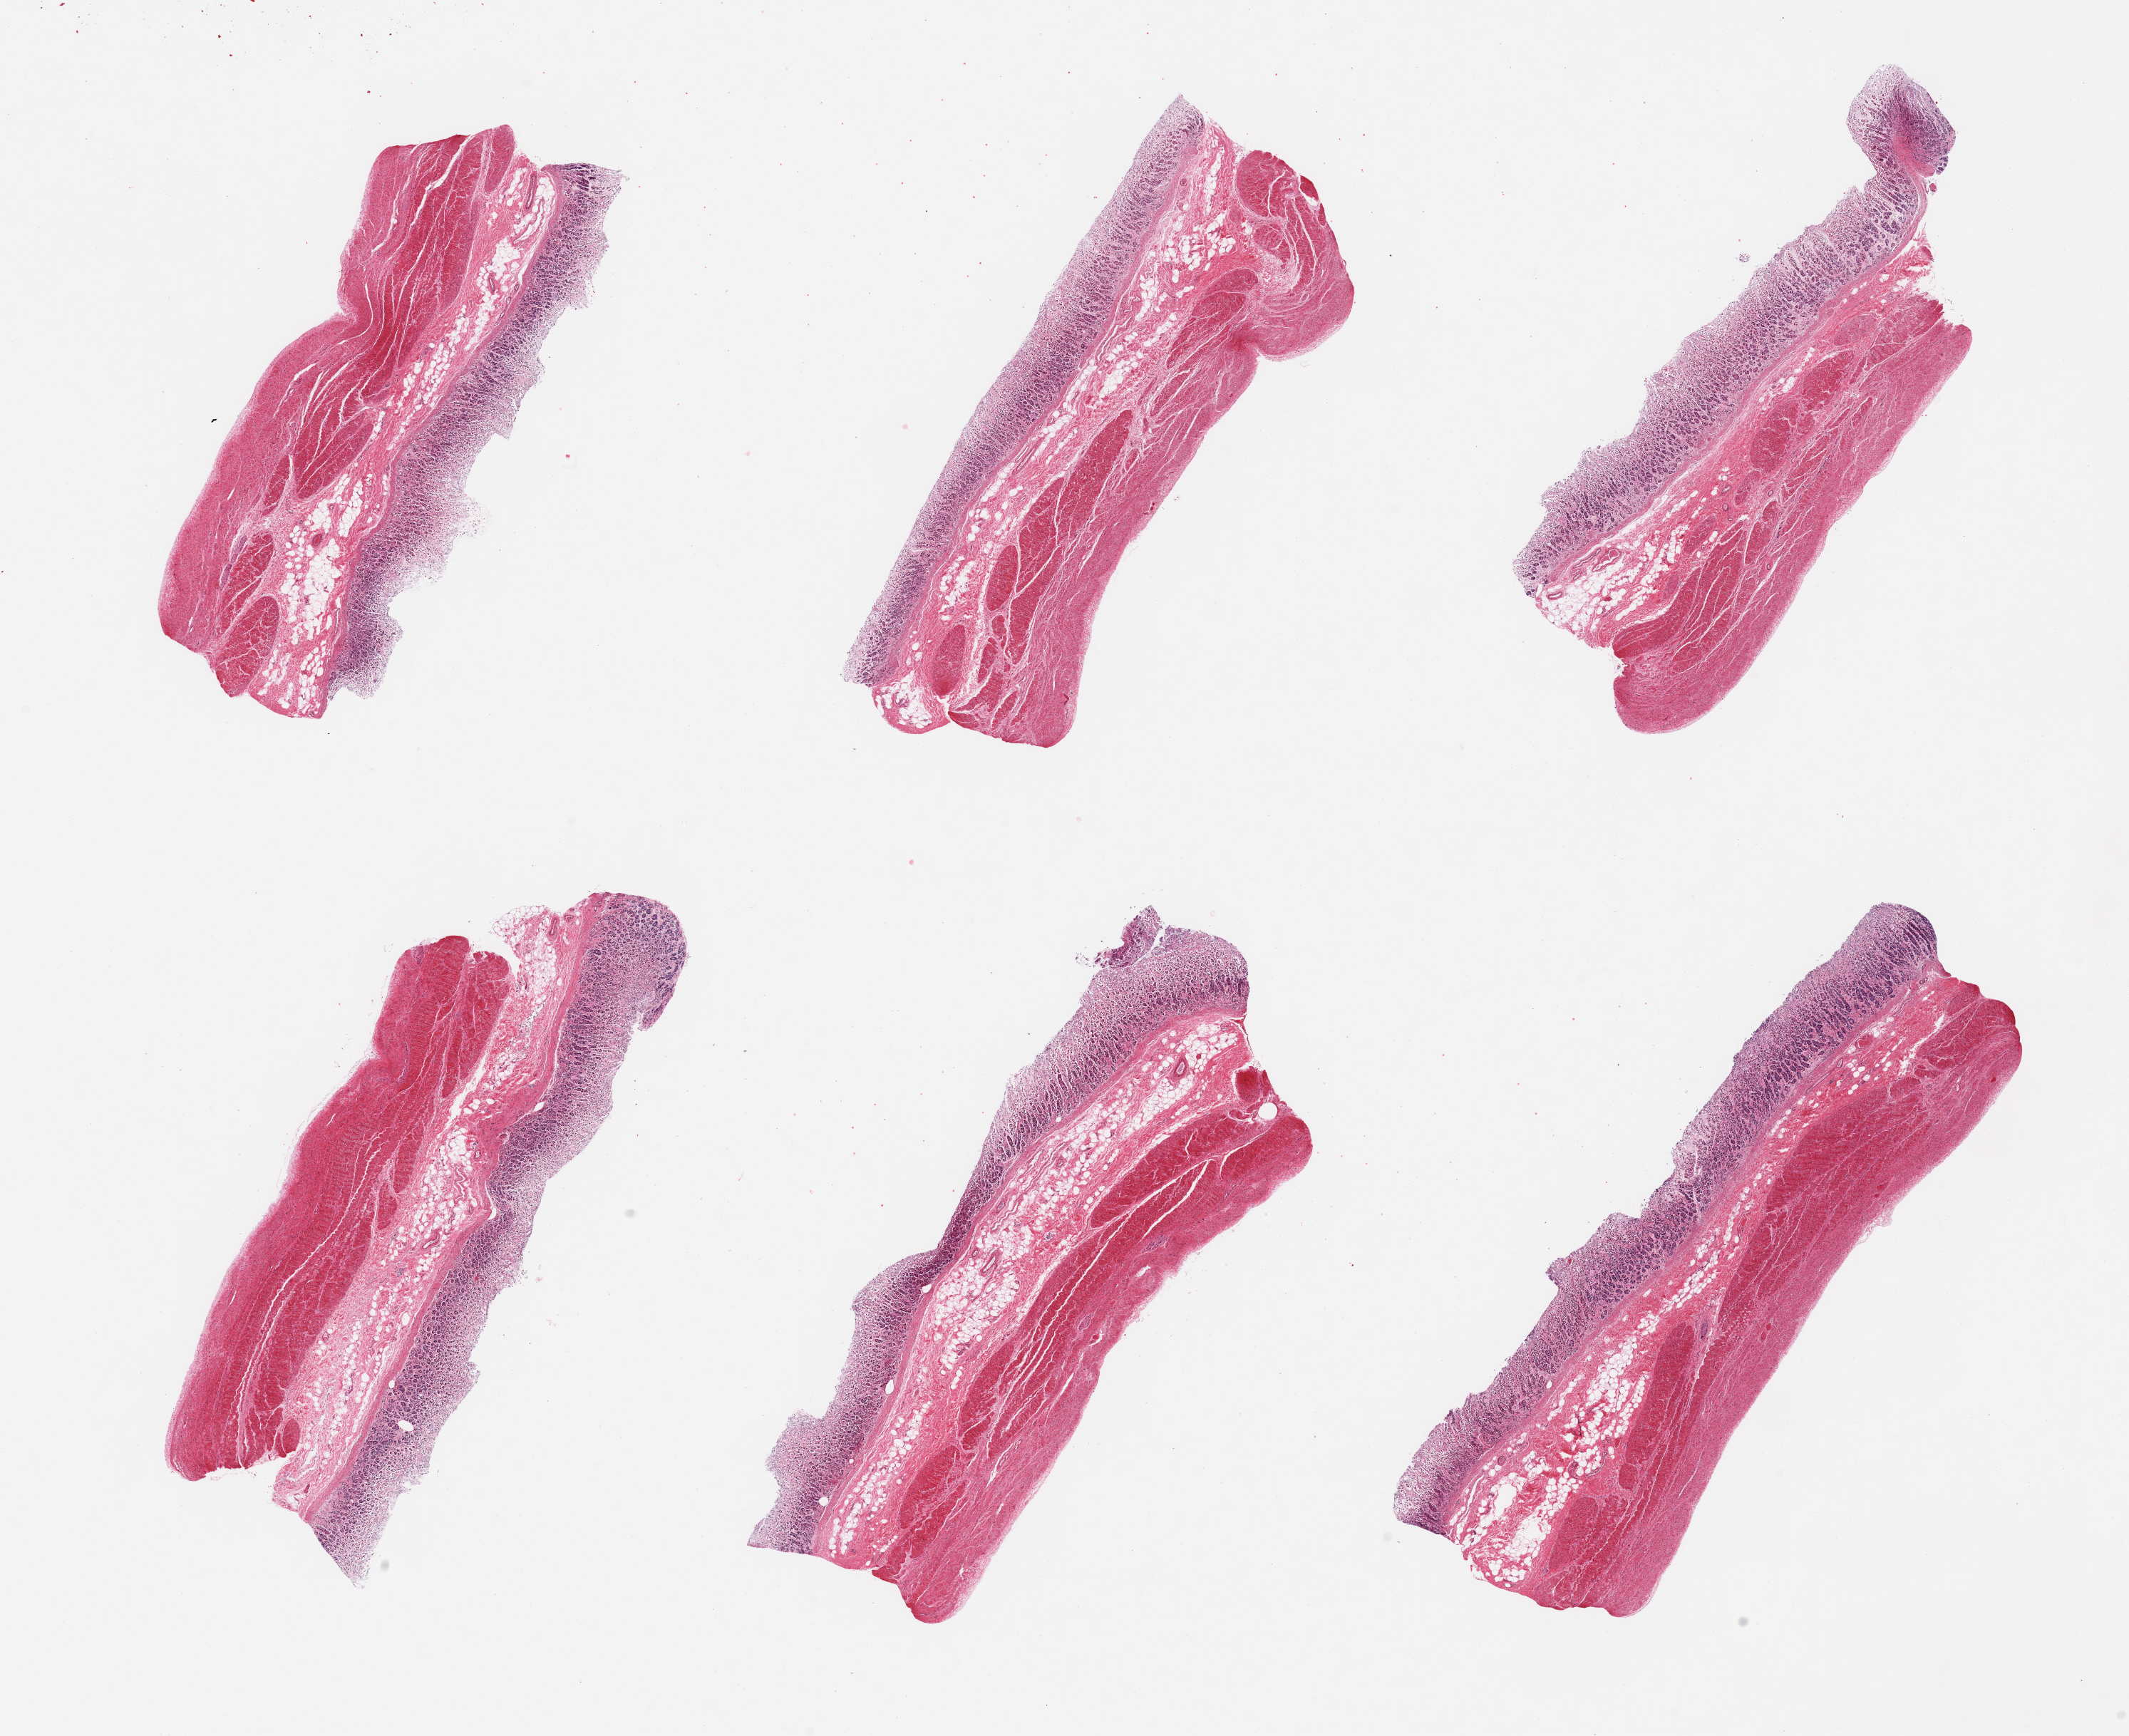
Hematoxylin and eosin (H&E) whole-slide image, shown as a low-resolution overview of the whole scanned area (about 23.6 x 19.3 mm), PAXgene-fixed, paraffin-embedded tissue, target tissue: stomach, donor tissue sample.
Reviewer comment on this tissue sample: 6 pieces, mucosa up to ~1mm, moderate-advanced autolysis.